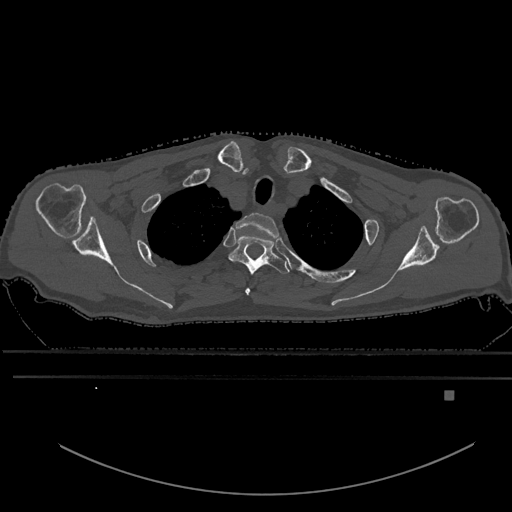
CT including the spine, one axial slice; position 503 of 969 along the scan axis; bone window (W 1800 / L 400 HU); 0.5 mm slice thickness; 512 × 512 image matrix. Patient: male, 82 years. Case-level facts recorded for this patient, not image findings: primary cancer: prostate; vertebrae with lytic lesions (as recorded): T11, T9, T8, T2.
Annotated regions visible in this slice (semi-automatically segmented with operator editing):
- T1 vertebra: box from (x=236, y=212) to (x=279, y=291) px
- T2 vertebra: (x=229, y=235)–(x=290, y=295)